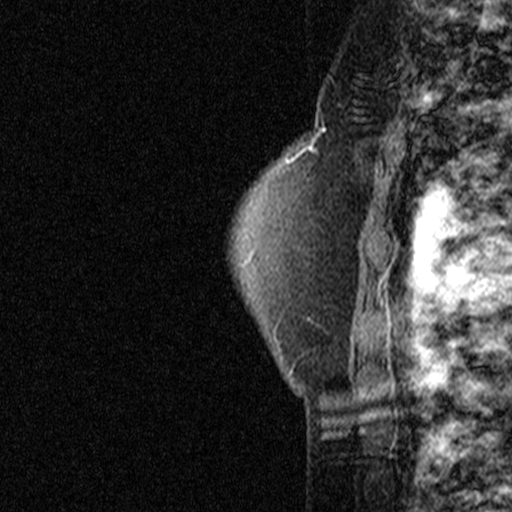
Breast MRI (dynamic contrast-enhanced), one sagittal slice; dynamic contrast-enhanced study with each time point stored as its own series, time point 2 of 3 at this slice position (early post-contrast, ordered by acquisition time); 1.5 T; TE 4.5 ms, TR 11 ms; 3 mm slice thickness; 512 × 512 image matrix, field of view 200 × 200 mm. Female patient, age 49 years. Case-level facts recorded for this patient, not image findings: setting: breast cancer imaged before/during neoadjuvant chemotherapy; receptor status: triple-negative.
Annotated regions visible in this slice (semi-automatically segmented with operator editing):
- analysis volume of interest (the breast-tissue region the enhancement analysis was run in; not a lesion): bounding box <276,94,369,181> (left, top, right, bottom; pixels)
- tumour enhancement mask (voxels above the 90 % enhancement threshold inside the analysis volume of interest): <318,128,326,131>